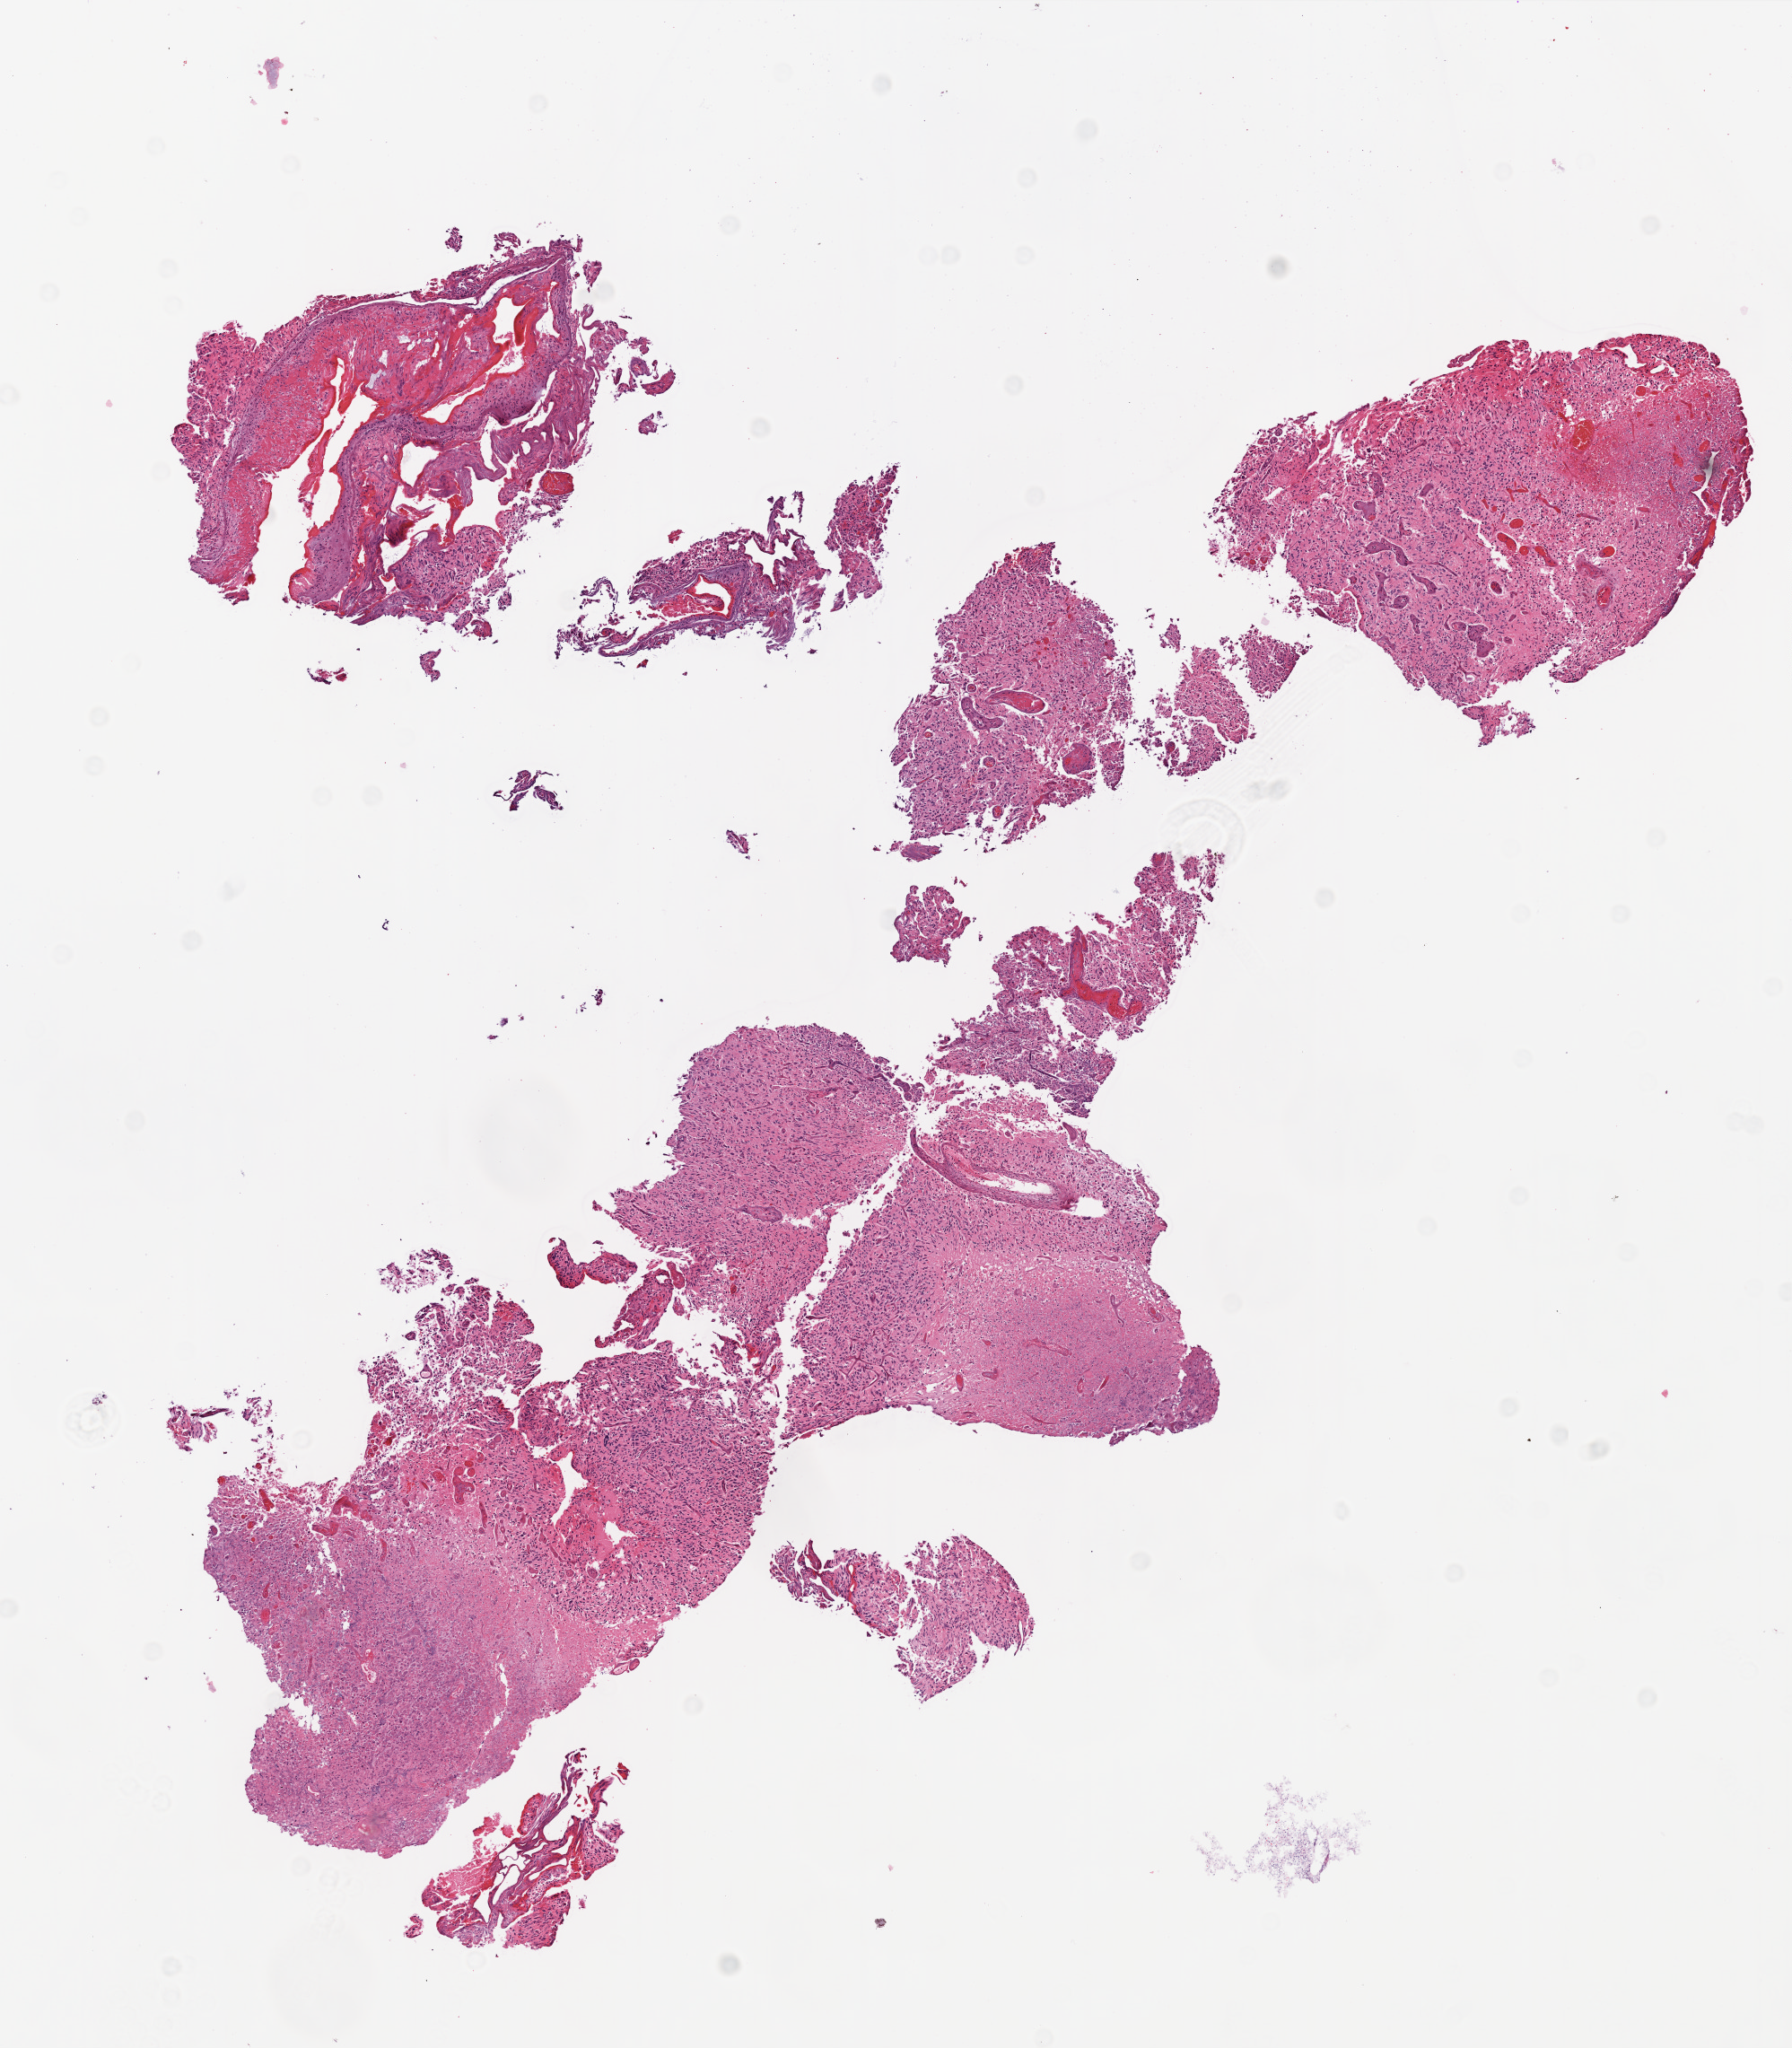
Whole-slide histology image, Hematoxylin and eosin (H&E) stained, low-resolution overview of the scanned area, about 8.0 x 9.1 mm (slide scanned at 20x), formalin-fixed paraffin-embedded (FFPE) diagnostic section, brain, primary tumour sample. Patient: male, age at initial diagnosis 76 years.
Diagnosis: Glioblastoma.